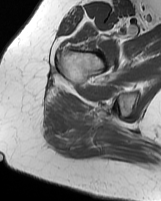
MRI of an extremity soft-tissue mass, one axial slice. Slice 49 of 70 in the series (ordered by position). MR volume resampled by the dataset authors to the PET/CT grid (not the native acquisition matrix). 161 × 201 image matrix. Female patient. Case-level facts recorded for this patient, not image findings: histological type: synovial sarcoma; grade: intermediate; site of the primary tumour: right buttock.
Structures marked on this image (expert contour drawn on MRI and transferred to this co-registered scan by the dataset authors):
- gross tumour volume including surrounding oedema: box from (x=81, y=129) to (x=95, y=139) px